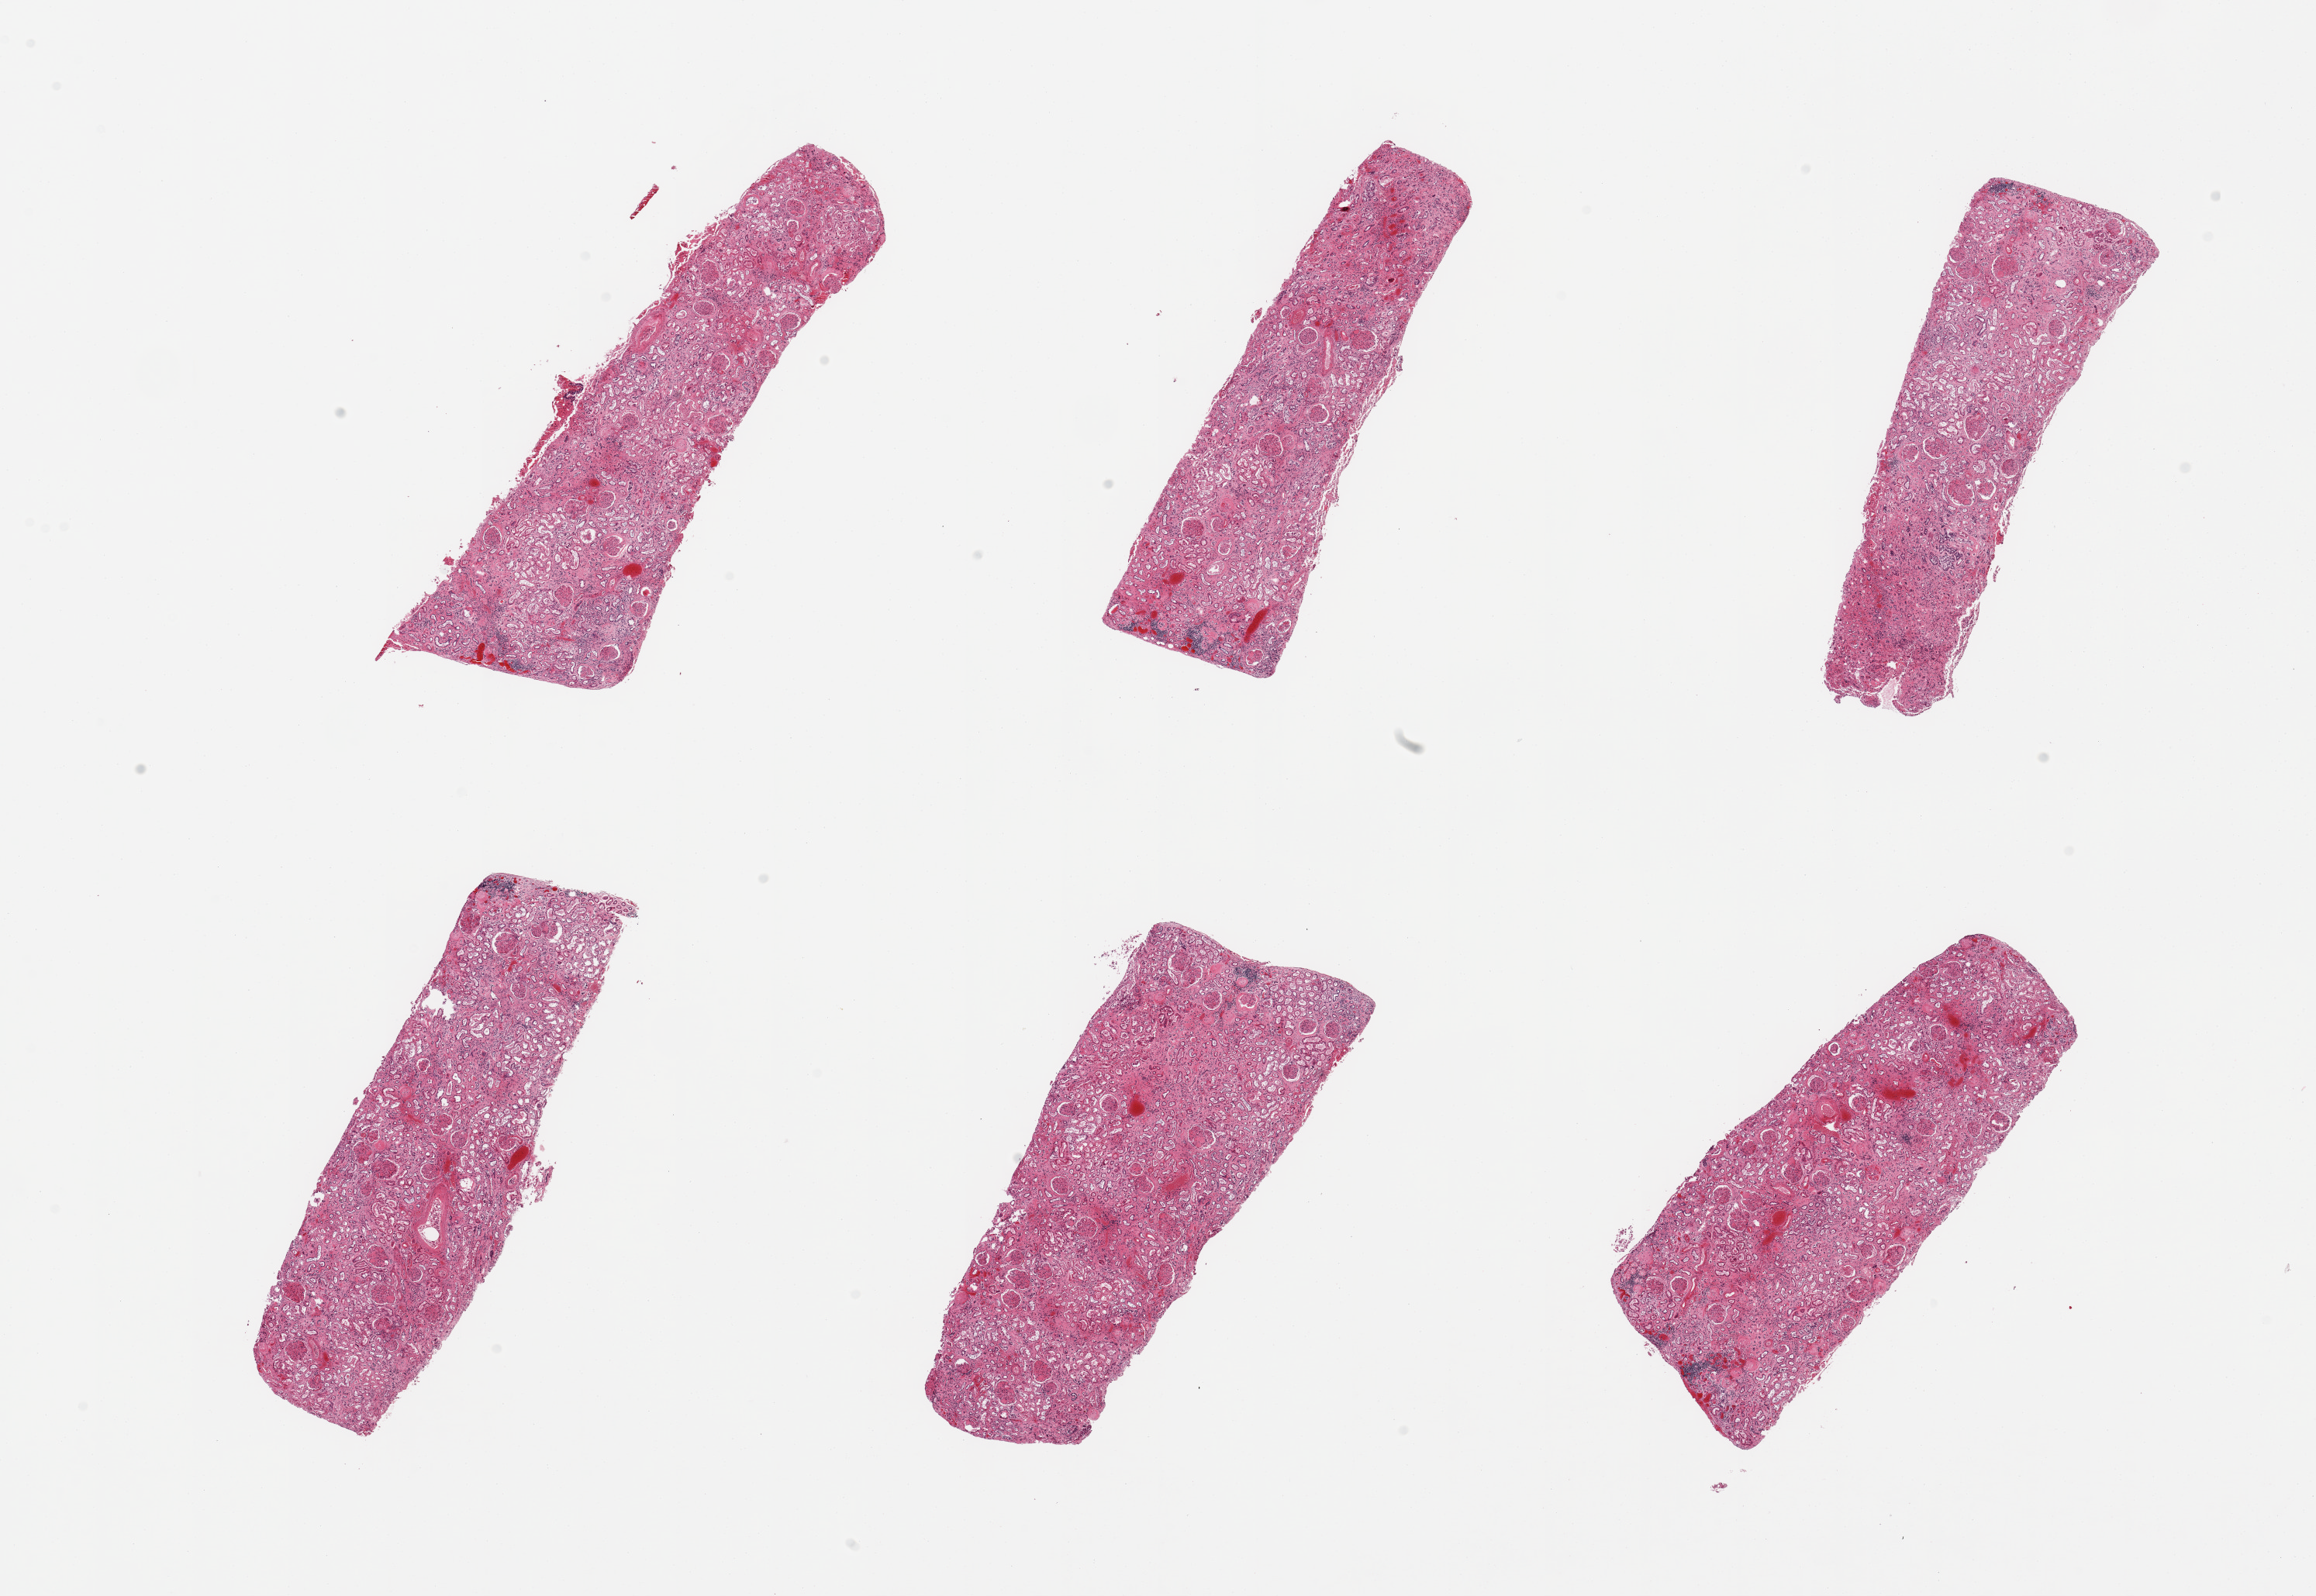
Whole-slide image, H&E stain — low-resolution overview of the scanned area, about 23.6 x 16.3 mm (acquisition: 20x scan), PAXgene-fixed paraffin-embedded (PFPE) section, section of renal cortex (target tissue), tissue donor sample. Donor: female.
Review note (as recorded): 6 pieces; diffuse nodular diabetic glomerulosclerosis; arterio and arteriolonephrosclerosis; congestion.